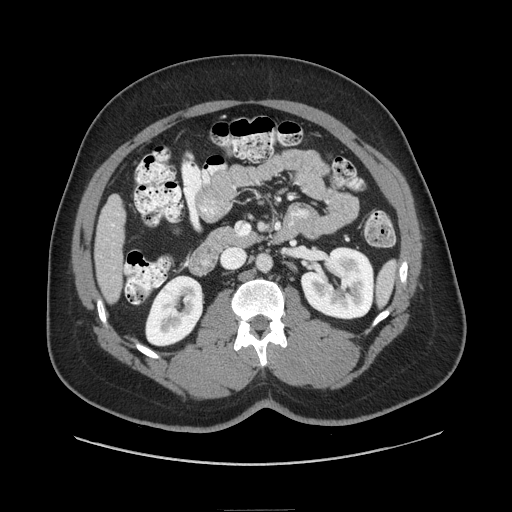
Contrast-enhanced abdominal CT (liver protocol), one axial slice. Slice 21 of 87 in the series (ordered by position). Soft-tissue window (W 400 / L 40 HU). 2.5 mm slice thickness. 512 × 512 image matrix. From the clinical record (not read from this slice): diagnosis: hepatocellular carcinoma (patient treated with transarterial chemoembolisation; whether this scan precedes or follows treatment is not stated here); TNM stage (as recorded): Stage-II; Child-Pugh class: A.
Annotated regions visible in this slice (semi-automatic segmentation, software-assisted and operator-edited):
- liver parenchyma outside the tumour (the mass and vessels are separate outlines, so this box may not span the whole liver): box from (x=94, y=194) to (x=124, y=302) px
- liver vessels: (x=112, y=224)–(x=114, y=227)